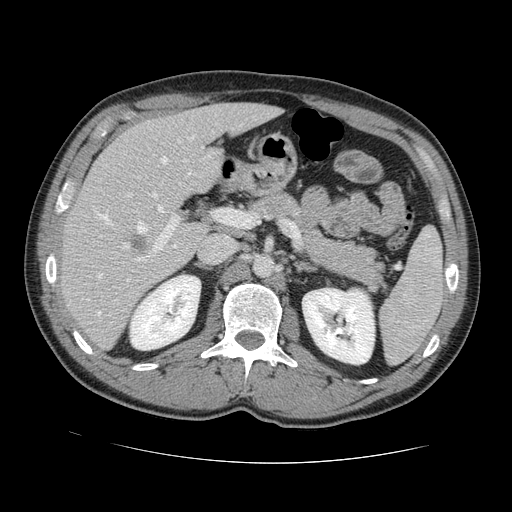
Contrast-enhanced abdominal CT, one axial slice. Slice 77 of 131 in the series (ordered by position). 120 kVp. Soft-tissue window (W 400 / L 40 HU). 2.5 mm slice thickness. 512 × 512 image matrix, field of view 380 × 380 mm. Male patient, age 40 years. From the clinical record (not read from this slice): diagnosis: colorectal cancer liver metastases, imaged before liver resection; multiple liver metastases: yes; largest metastasis: 2.9 cm; disease in both lobes: yes.
Outlined on this slice (manually delineated by an expert):
- hepatic veins: box from (x=97, y=137) to (x=191, y=316) px
- liver: (x=63, y=104)–(x=276, y=347)
- planned liver remnant (the part of the liver to remain after resection): (x=106, y=104)–(x=276, y=198)
- portal vein (with intrahepatic branches): (x=135, y=192)–(x=234, y=262)
- liver metastasis: (x=130, y=234)–(x=149, y=254)